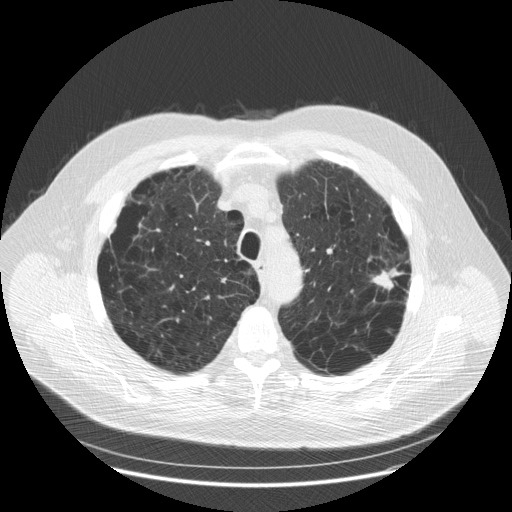
Low-dose screening chest CT, one axial slice. Position 138 of 179 along the scan axis. Reconstruction kernel STANDARD. Lung window (W 1500 / L -600 HU). 512 × 512 image matrix, field of view 404 × 404 mm.
Structures marked on this image (expert manual segmentation):
- lesion 1 (tumor, upper lobe of left lung): bounding box <371,268,404,291> (left, top, right, bottom; pixels)